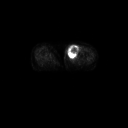
FDG PET of an extremity soft-tissue mass (from a PET/CT study), one axial slice. Slice 40 of 91 in the series (ordered by position). 3.27 mm slice thickness. 128 × 128 image matrix, field of view 700 × 700 mm. Female patient, age 74 years. Case-level facts recorded for this patient, not image findings: histological type: pleomorphic leiomyosarcoma; grade: high; site of the primary tumour: left thigh.
Structures marked on this image (expert contour drawn on MRI and transferred to this co-registered scan by the dataset authors):
- gross tumour volume including surrounding oedema: bounding box <66,43,80,61> (left, top, right, bottom; pixels)
- gross tumour volume (mass): <67,43,80,59>